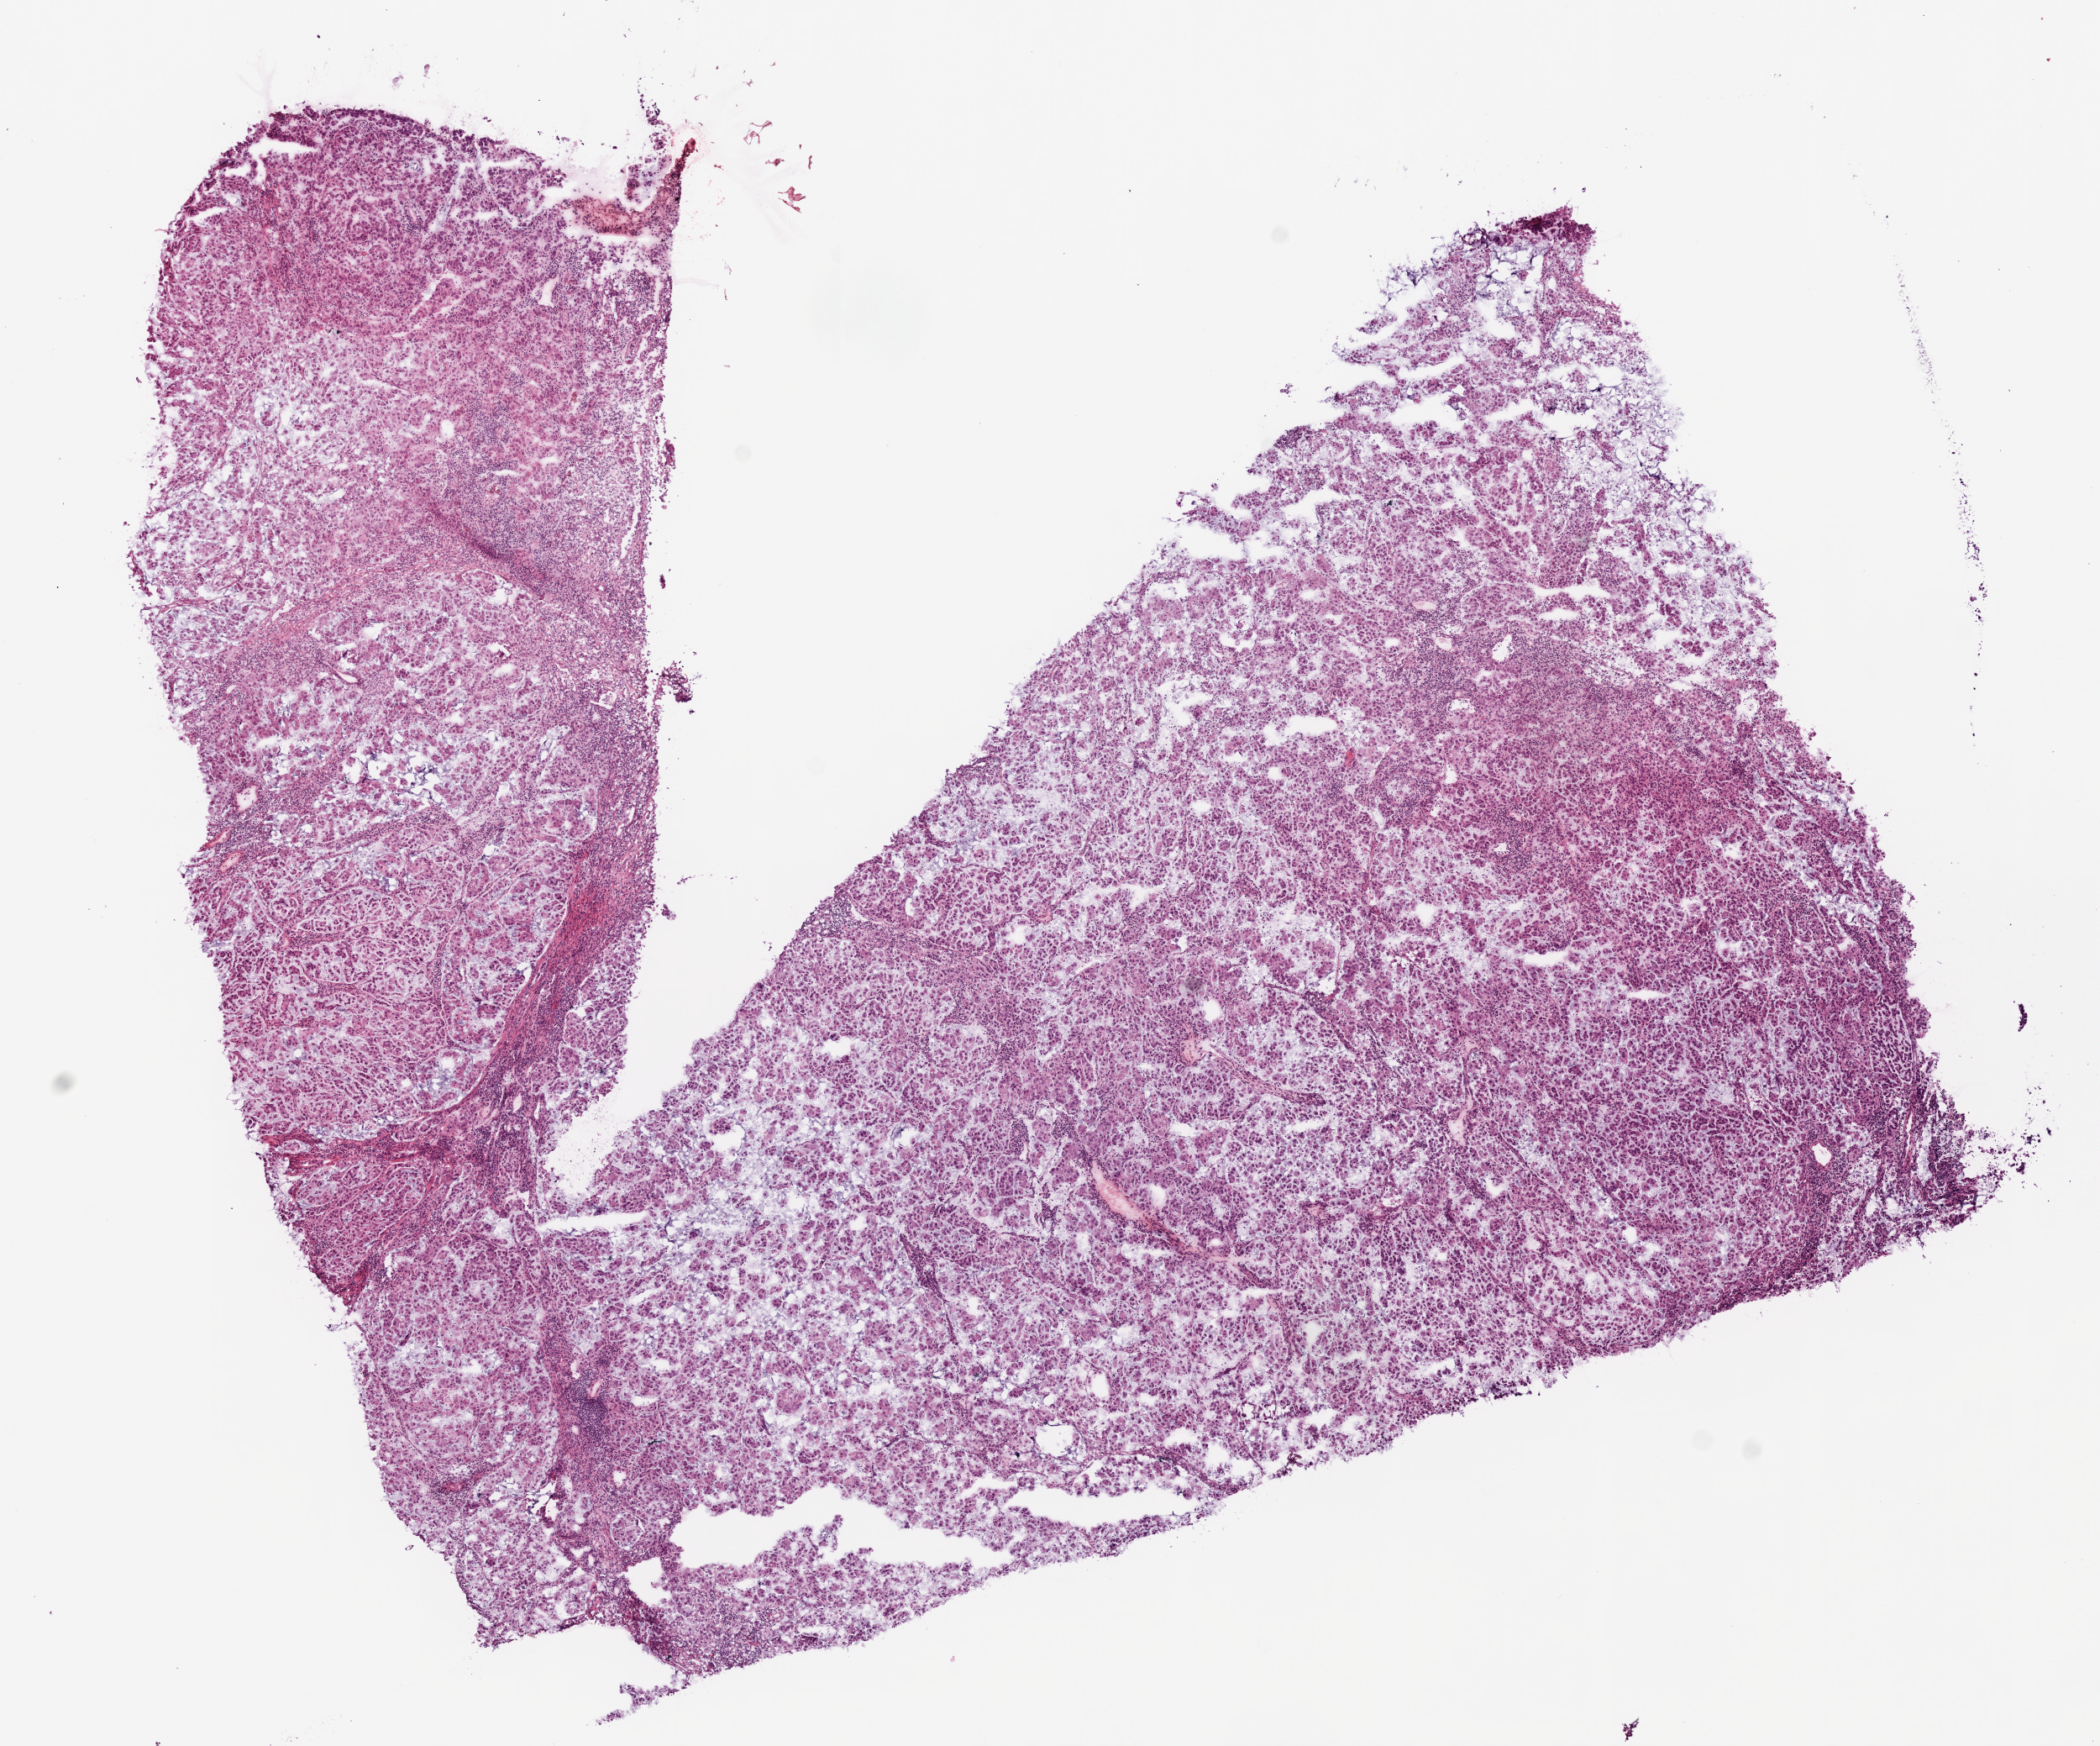
Digitized Hematoxylin and eosin (H&E) stained tissue section (whole slide), low-resolution overview of the scanned area, about 10.0 x 8.3 mm (slide scanned at 20x); frozen section from the top of the tissue portion; sample: primary tumour, lung. Female patient; age at initial diagnosis 68 years. Slide review estimates, as recorded: tumour cells 95%, tumour nuclei 70%, normal cells 0%, stromal cells 5%, necrosis 0%.
• AJCC pathologic stage: IIB (4th edition)
• histologic diagnosis: Adenocarcinoma, NOS (upper lobe, lung)
• laterality: left